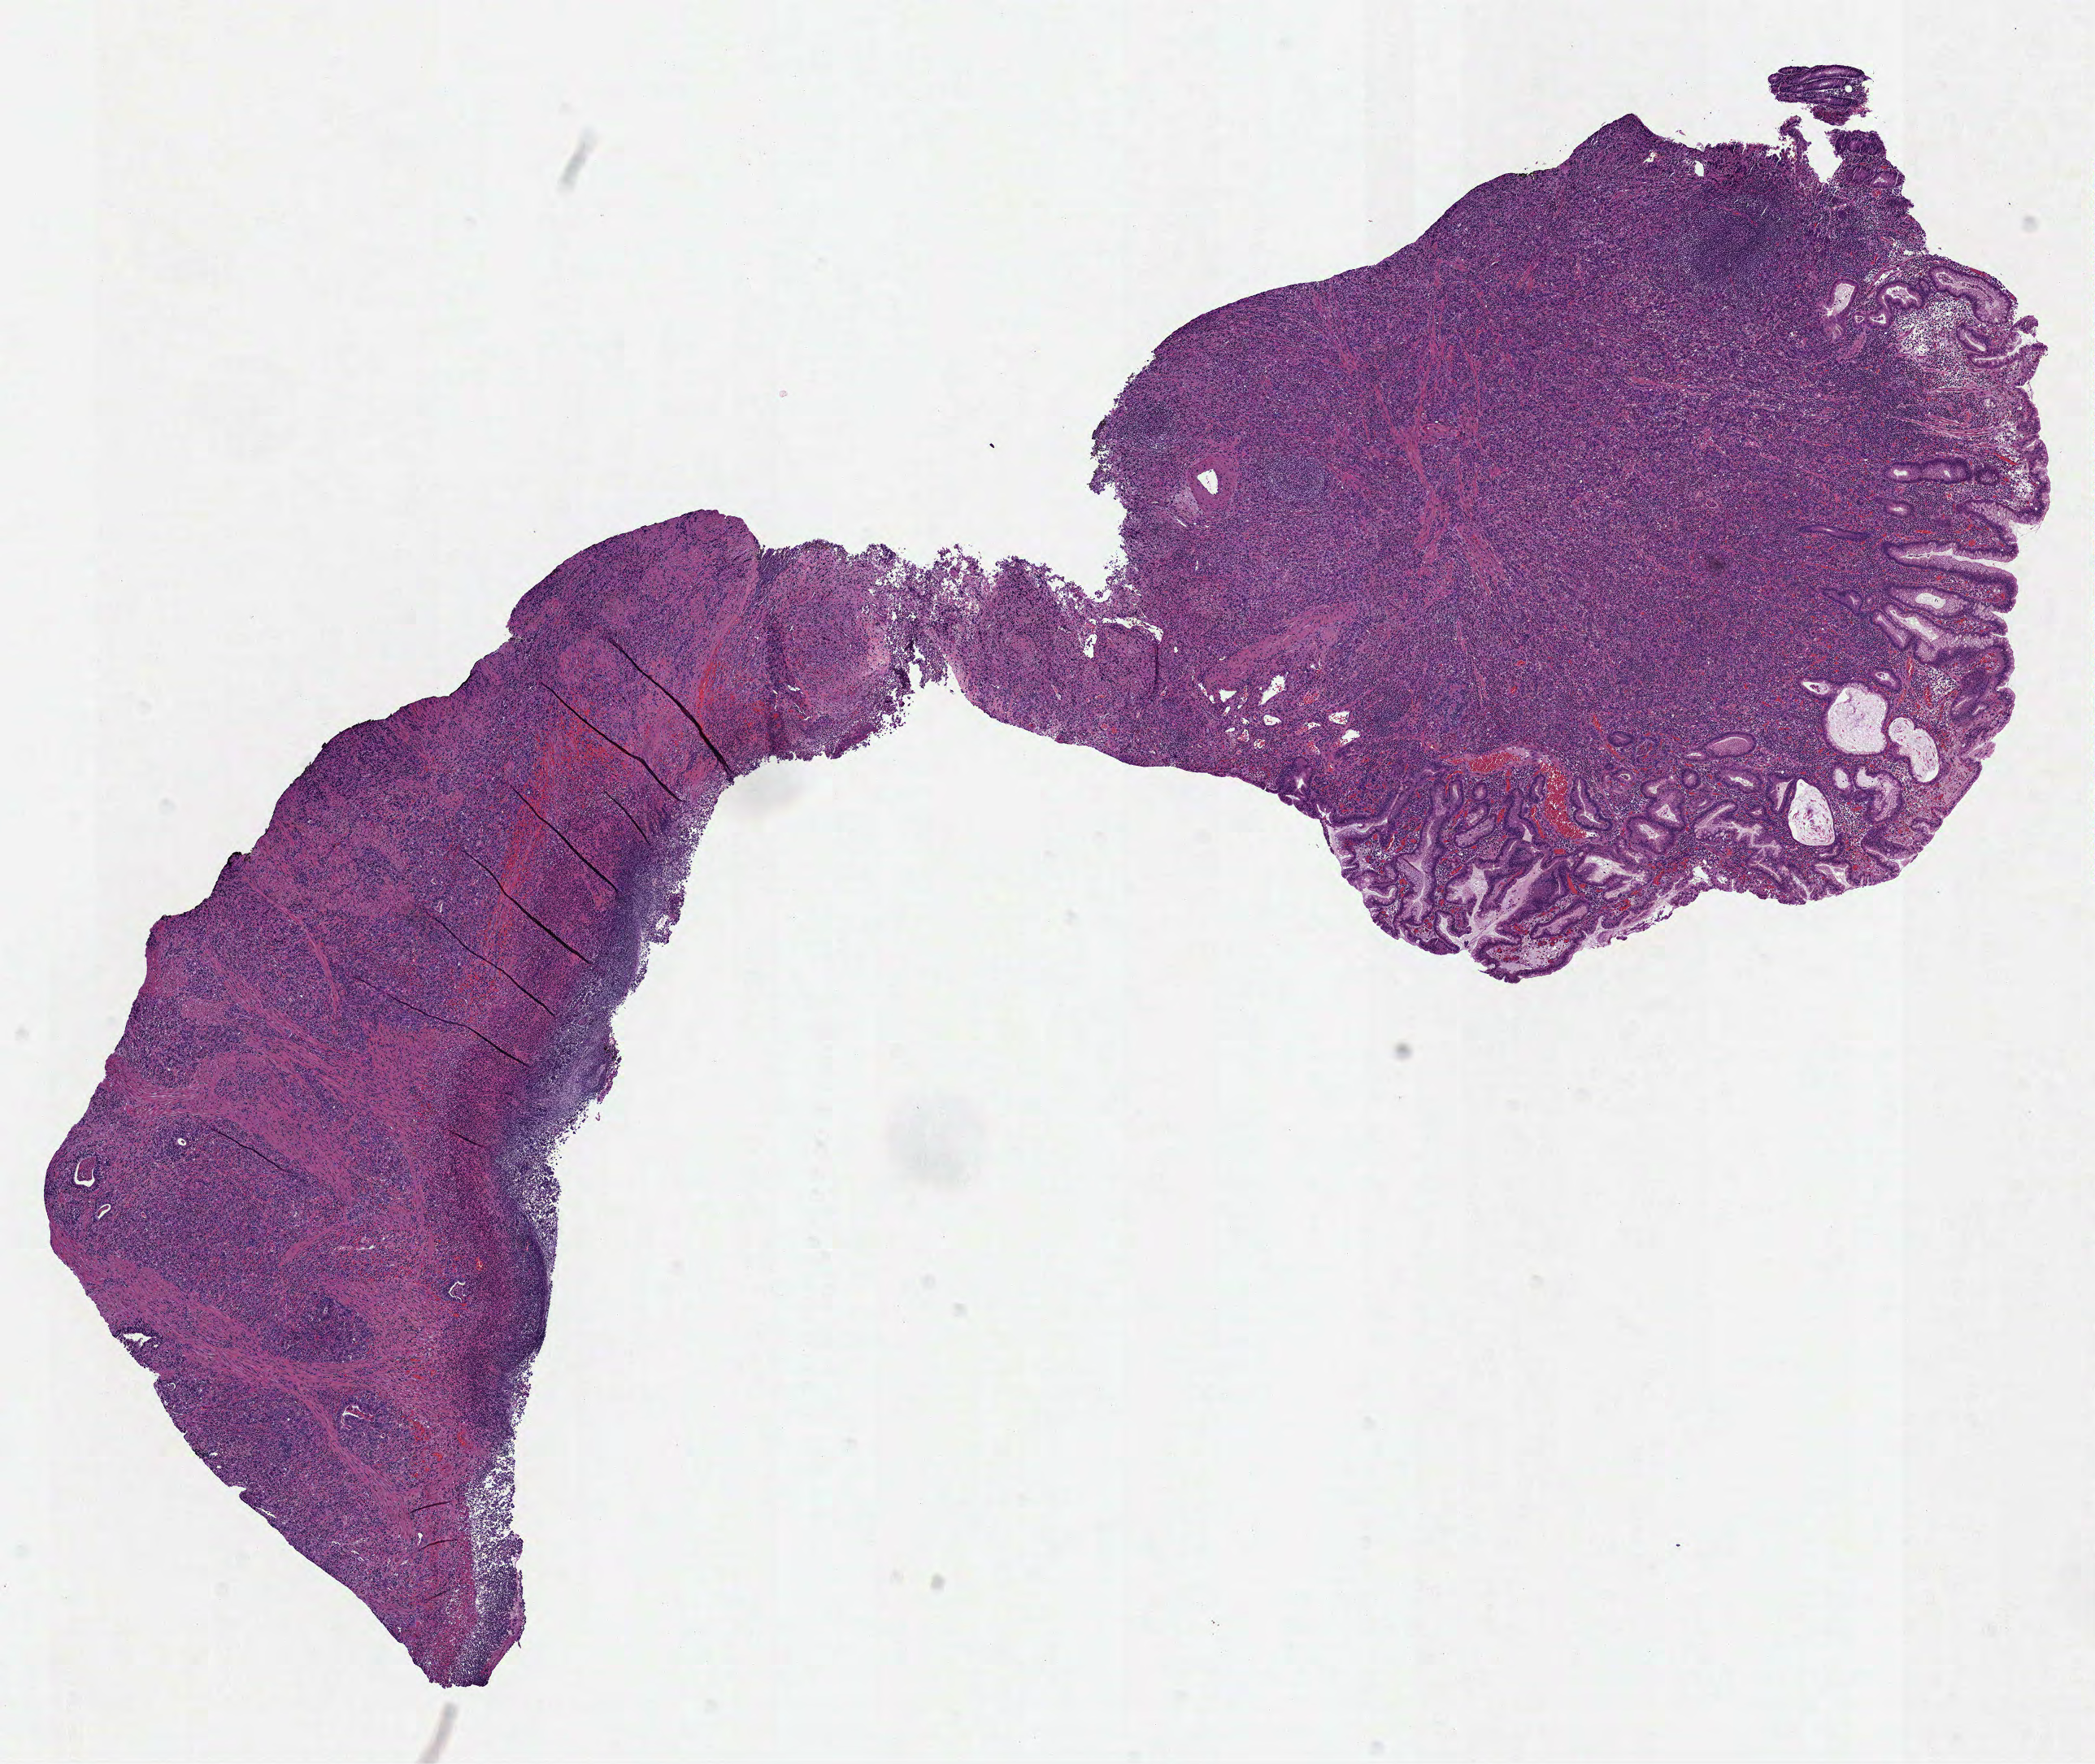
Digitized H&E-stained tissue section (whole slide) — whole scanned area (about 10.4 x 8.8 mm, from a 40x scan) shown as a low-resolution overview; formalin-fixed paraffin-embedded (FFPE) diagnostic section; stomach, primary tumour sample. Male, age 77 years at initial diagnosis. Histologic grade: G3 (poorly differentiated).
TNM: T4a N3a MX. Pathologic diagnosis: Carcinoma, diffuse type (body of stomach). Lymph nodes positive (case pathology): 14 of 30 examined. AJCC pathologic stage: IIIC (7th edition).